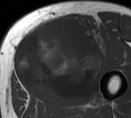
MRI of an extremity soft-tissue mass, one axial slice. Slice 34 of 55 in the series (ordered by position). MR volume resampled by the dataset authors to the PET/CT grid (not the native acquisition matrix). 3.27 mm slice thickness. 131 × 118 image matrix, field of view 128 × 115 mm. Male patient. From the clinical record (not read from this slice): histological type: pleiomorphic liposarcoma; grade: high; site of the primary tumour: left thigh.
Annotated regions visible in this slice (expert contour drawn on MRI and transferred to this co-registered scan by the dataset authors):
- gross tumour volume including surrounding oedema: box from (x=14, y=16) to (x=106, y=101) px
- gross tumour volume (mass): (x=14, y=16)–(x=103, y=102)